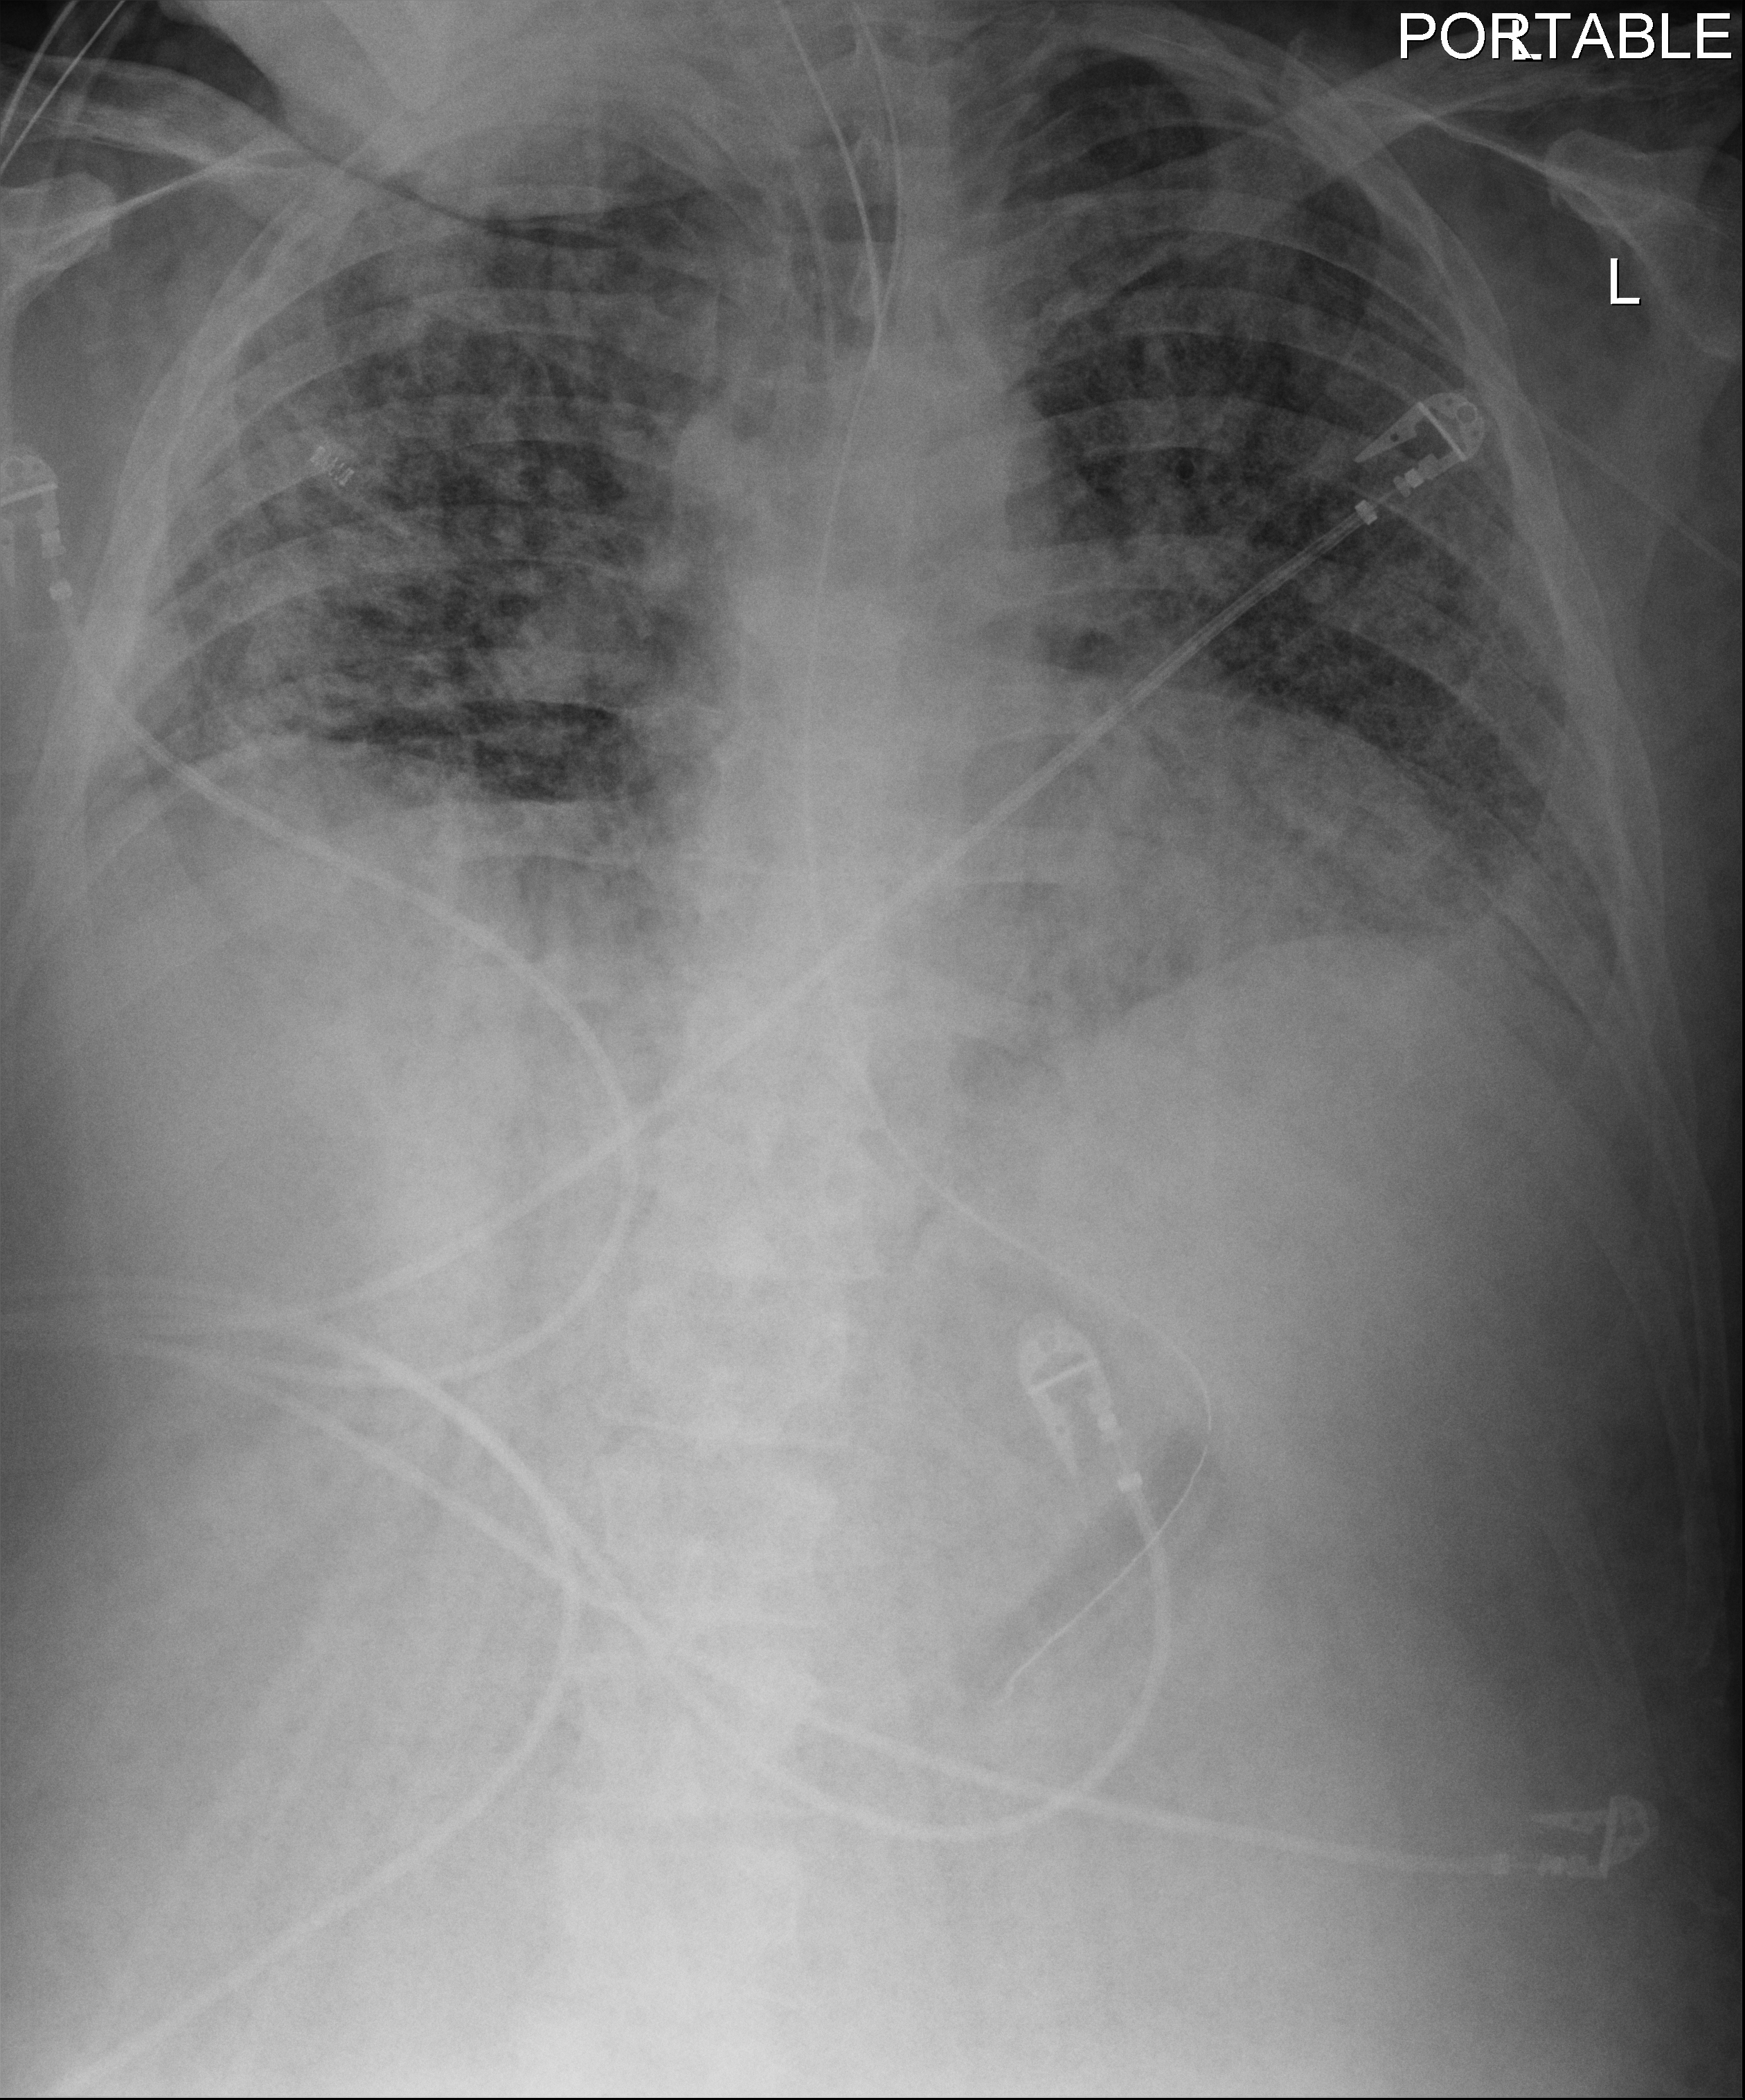
Chest X-ray (portable), anteroposterior (AP) projection. Patient hospitalised with COVID-19; male, aged 18–59 years.
Admission-level facts for this patient (not findings on this image; timing relative to this image not recorded):
- mechanically ventilated during this hospital stay: yes
- admitted to intensive care during this hospital stay: yes